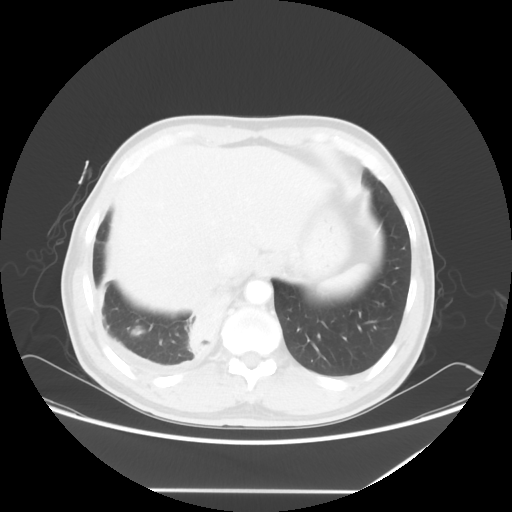
Chest CT, one axial slice; position 11 of 60 along the scan axis; lung window (W 1500 / L -600 HU); 5 mm slice thickness; 512 × 512 image matrix, field of view 419 × 419 mm. Patient: male, 48 years. Case-level facts recorded for this patient, not image findings: clinical TNM (as recorded): T3 N3 M1a.
Outlined on this slice (bounding box drawn by a radiologist):
- lung tumour (recorded histology: squamous cell carcinoma): bounding box [x1, y1, x2, y2] px = [183, 285, 233, 364]